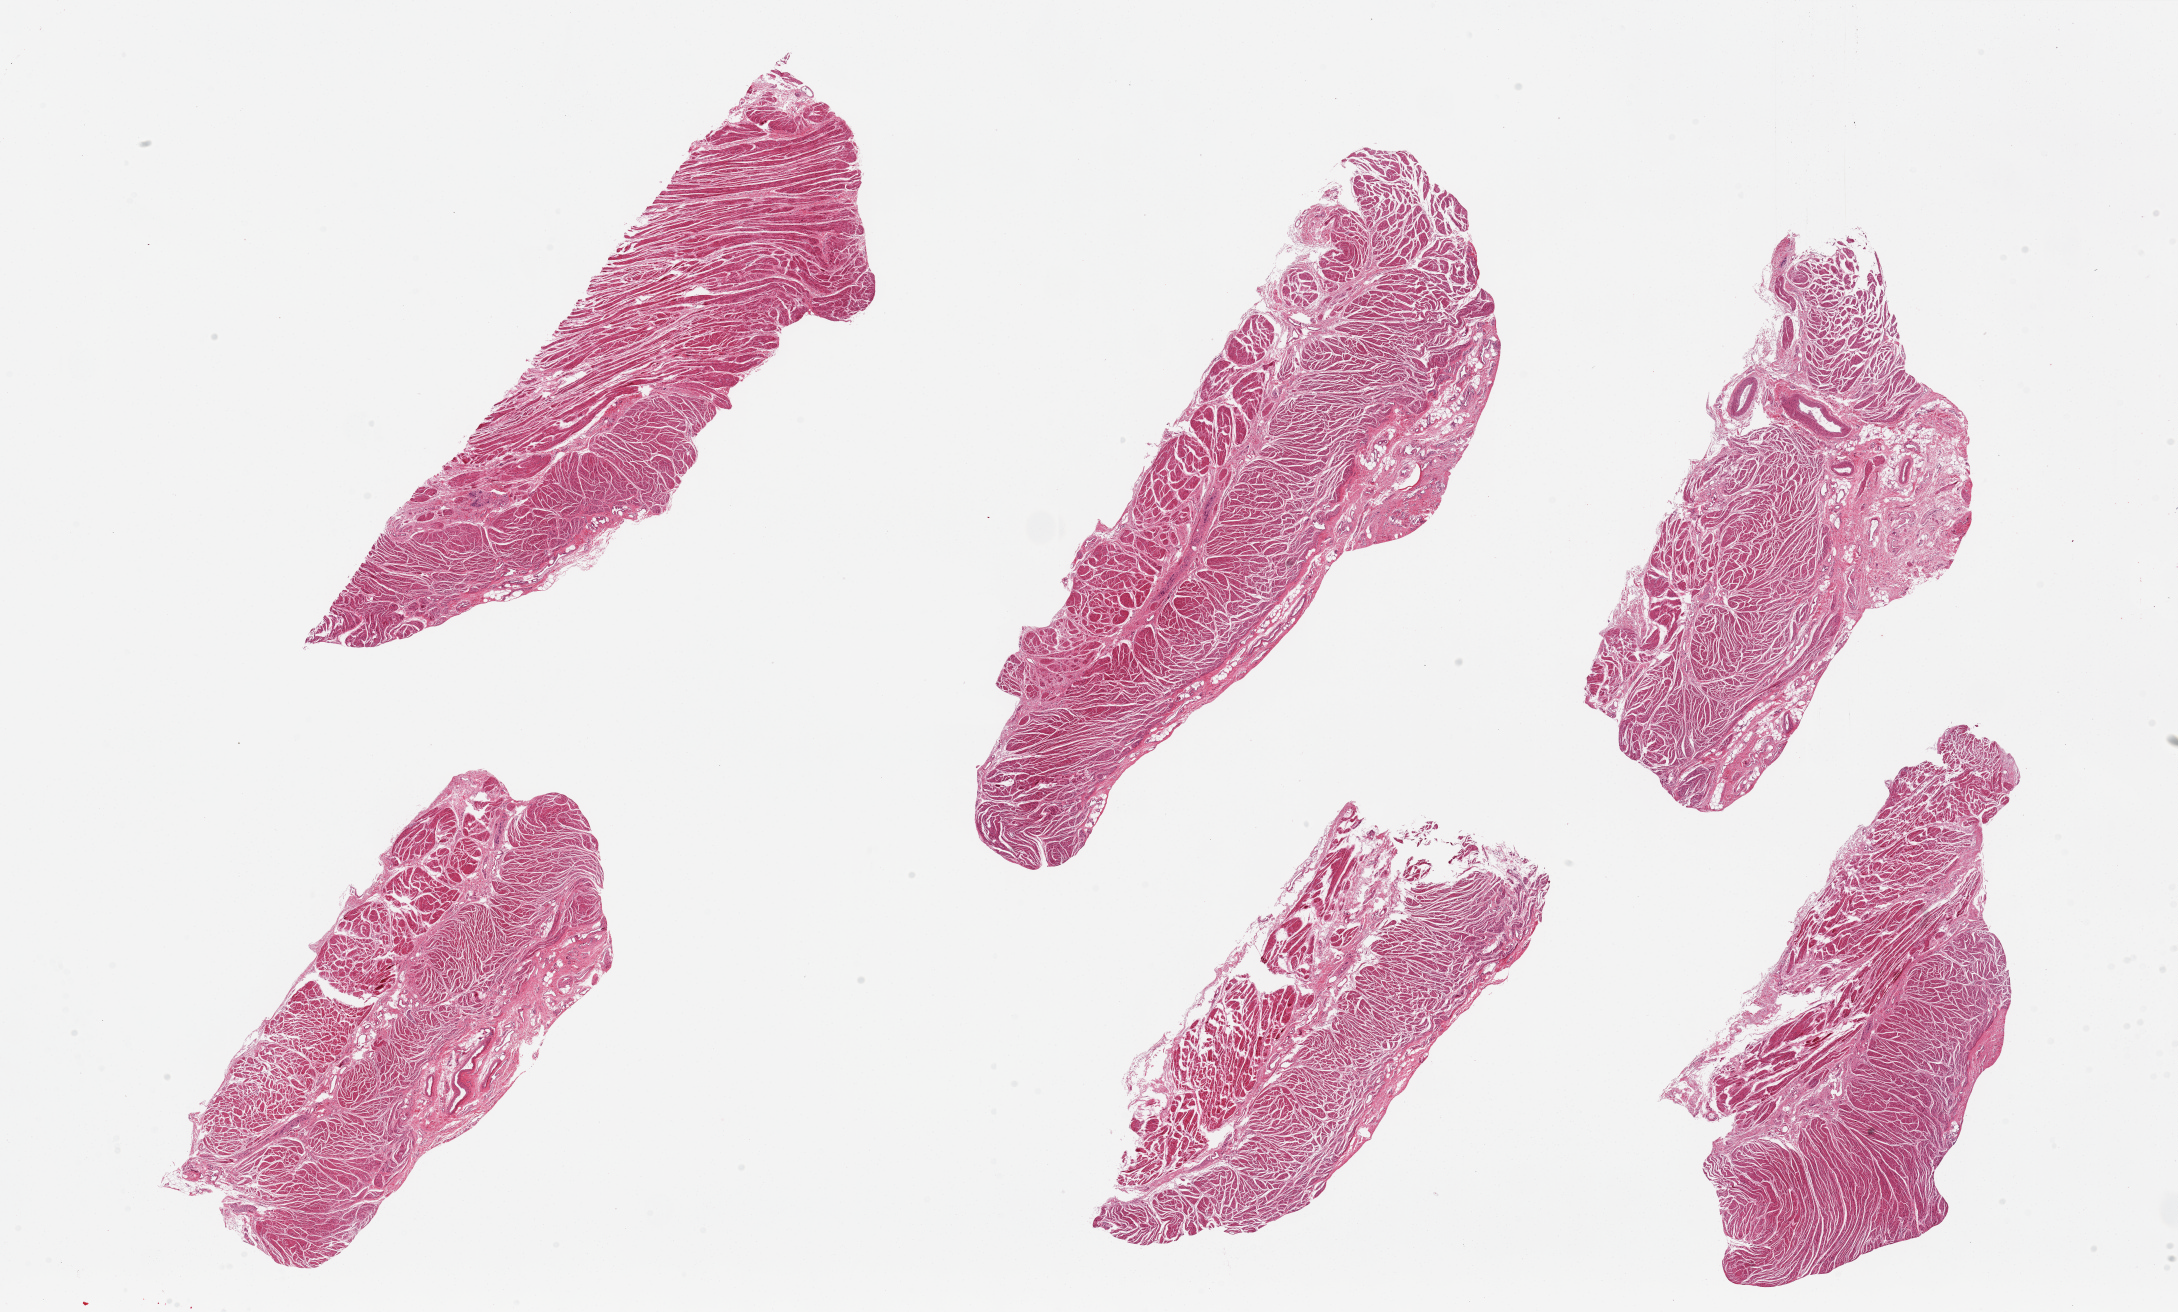
Haematoxylin and eosin whole-slide image, a low-resolution overview of the entire scanned area, about 34.5 x 20.8 mm (acquisition: 20x scan). PAXgene-fixed, paraffin-embedded tissue. Section of gastroesophageal junction (target tissue). Donor tissue sample. Donor: male.
- pathologist's review note for this sample: 6 pieces, from 8x3.5 to 11.5x3.5mm; well trimmed